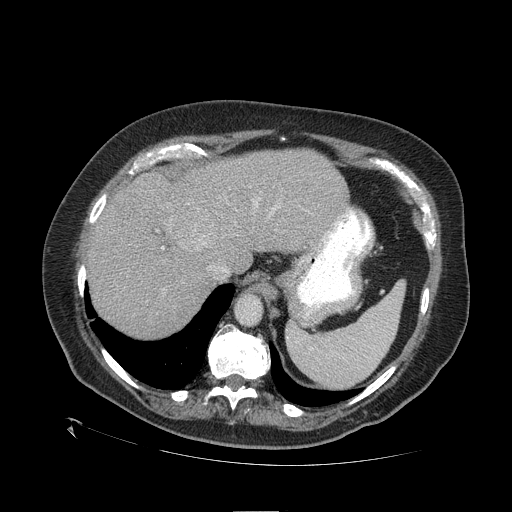
Contrast-enhanced abdominal CT (liver protocol), one axial slice; slice 83 of 109 in the series (ordered by position); one of 2 acquisitions stored at this slice position; soft-tissue window (W 400 / L 40 HU); 512 × 512 image matrix, field of view 460 × 460 mm. Case-level facts recorded for this patient, not image findings: diagnosis: hepatocellular carcinoma (patient treated with transarterial chemoembolisation; whether this scan precedes or follows treatment is not stated here); TNM stage (as recorded): Stage-I; Child-Pugh class: A; tumour differentiation: no biopsy; tumour nodularity: uninodular.
Outlined on this slice (semi-automatic segmentation, software-assisted and operator-edited):
- liver parenchyma outside the tumour (the mass and vessels are separate outlines, so this box may not span the whole liver): bounding box <88,150,348,338> (left, top, right, bottom; pixels)
- mass: <164,201,221,252>
- liver vessels: <162,198,343,249>